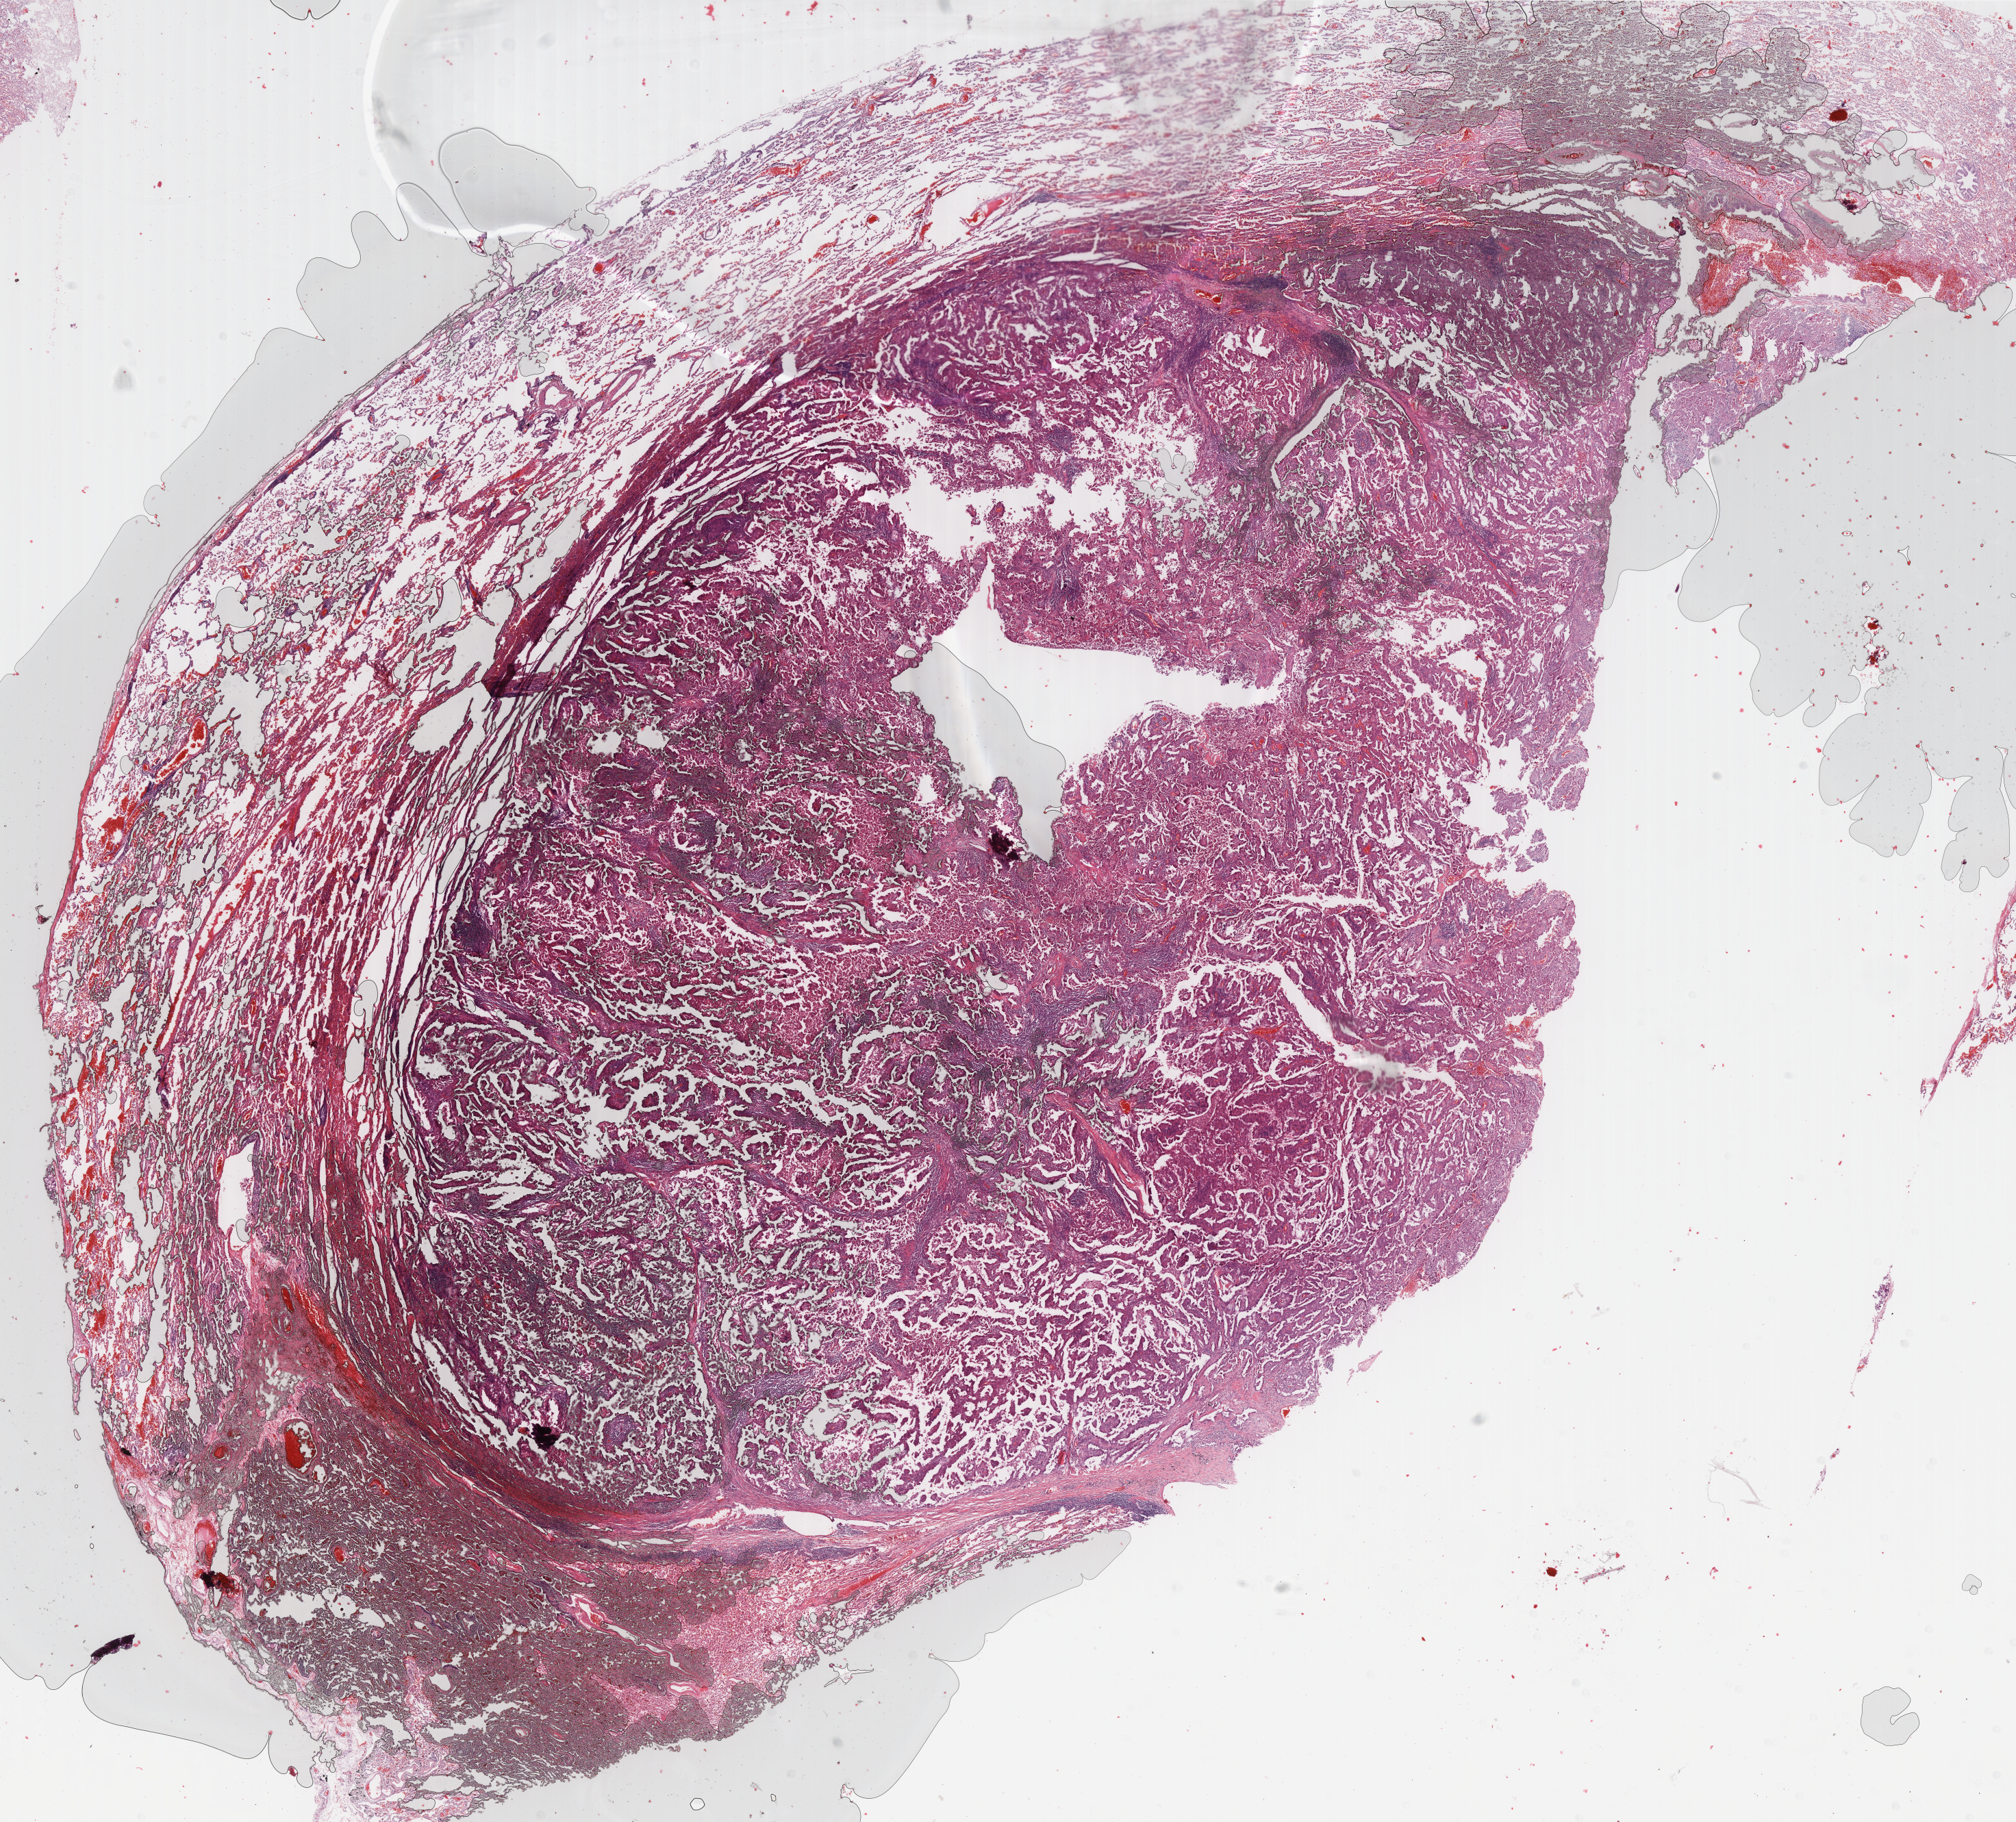
Digitized Hematoxylin and eosin (H&E) stained tissue section (whole slide) — a low-resolution overview of the entire scanned area, about 23.7 x 21.4 mm; FFPE section; sample: primary tumour, lung. Female, age 71 years at initial diagnosis.
Histologic diagnosis: Adenocarcinoma with mixed subtypes (lower lobe, lung). AJCC pathologic stage: IIB (6th edition).